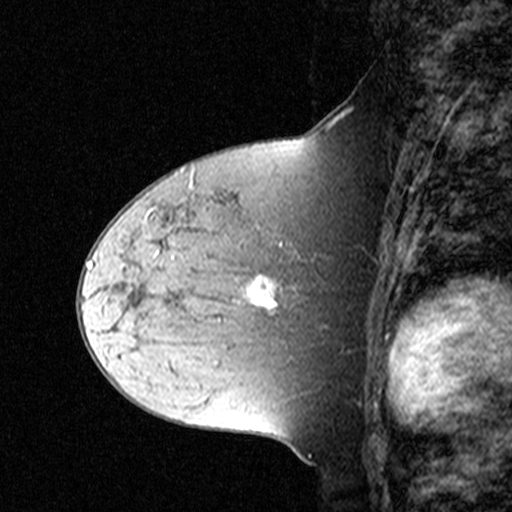
Breast MRI (dynamic contrast-enhanced), one sagittal slice; position 21 of 44 along the scan axis; dynamic contrast-enhanced study with each time point stored as its own series, time point 2 of 3 at this slice position (early post-contrast, ordered by acquisition time); 1.5 T; TE 4.5 ms, TR 11 ms; 512 × 512 image matrix, field of view 200 × 200 mm. Female patient, age 44 years. From the clinical record (not read from this slice): setting: breast cancer imaged before/during neoadjuvant chemotherapy; receptor status: triple-negative.
Outlined on this slice (semi-automatic segmentation, software-assisted and operator-edited):
- analysis volume of interest (the breast-tissue region the enhancement analysis was run in; not a lesion): bounding box (x1, y1, x2, y2) in pixels: (132, 212, 309, 331)
- tumour enhancement mask (voxels above the 90 % enhancement threshold inside the analysis volume of interest): (250, 275, 277, 311)